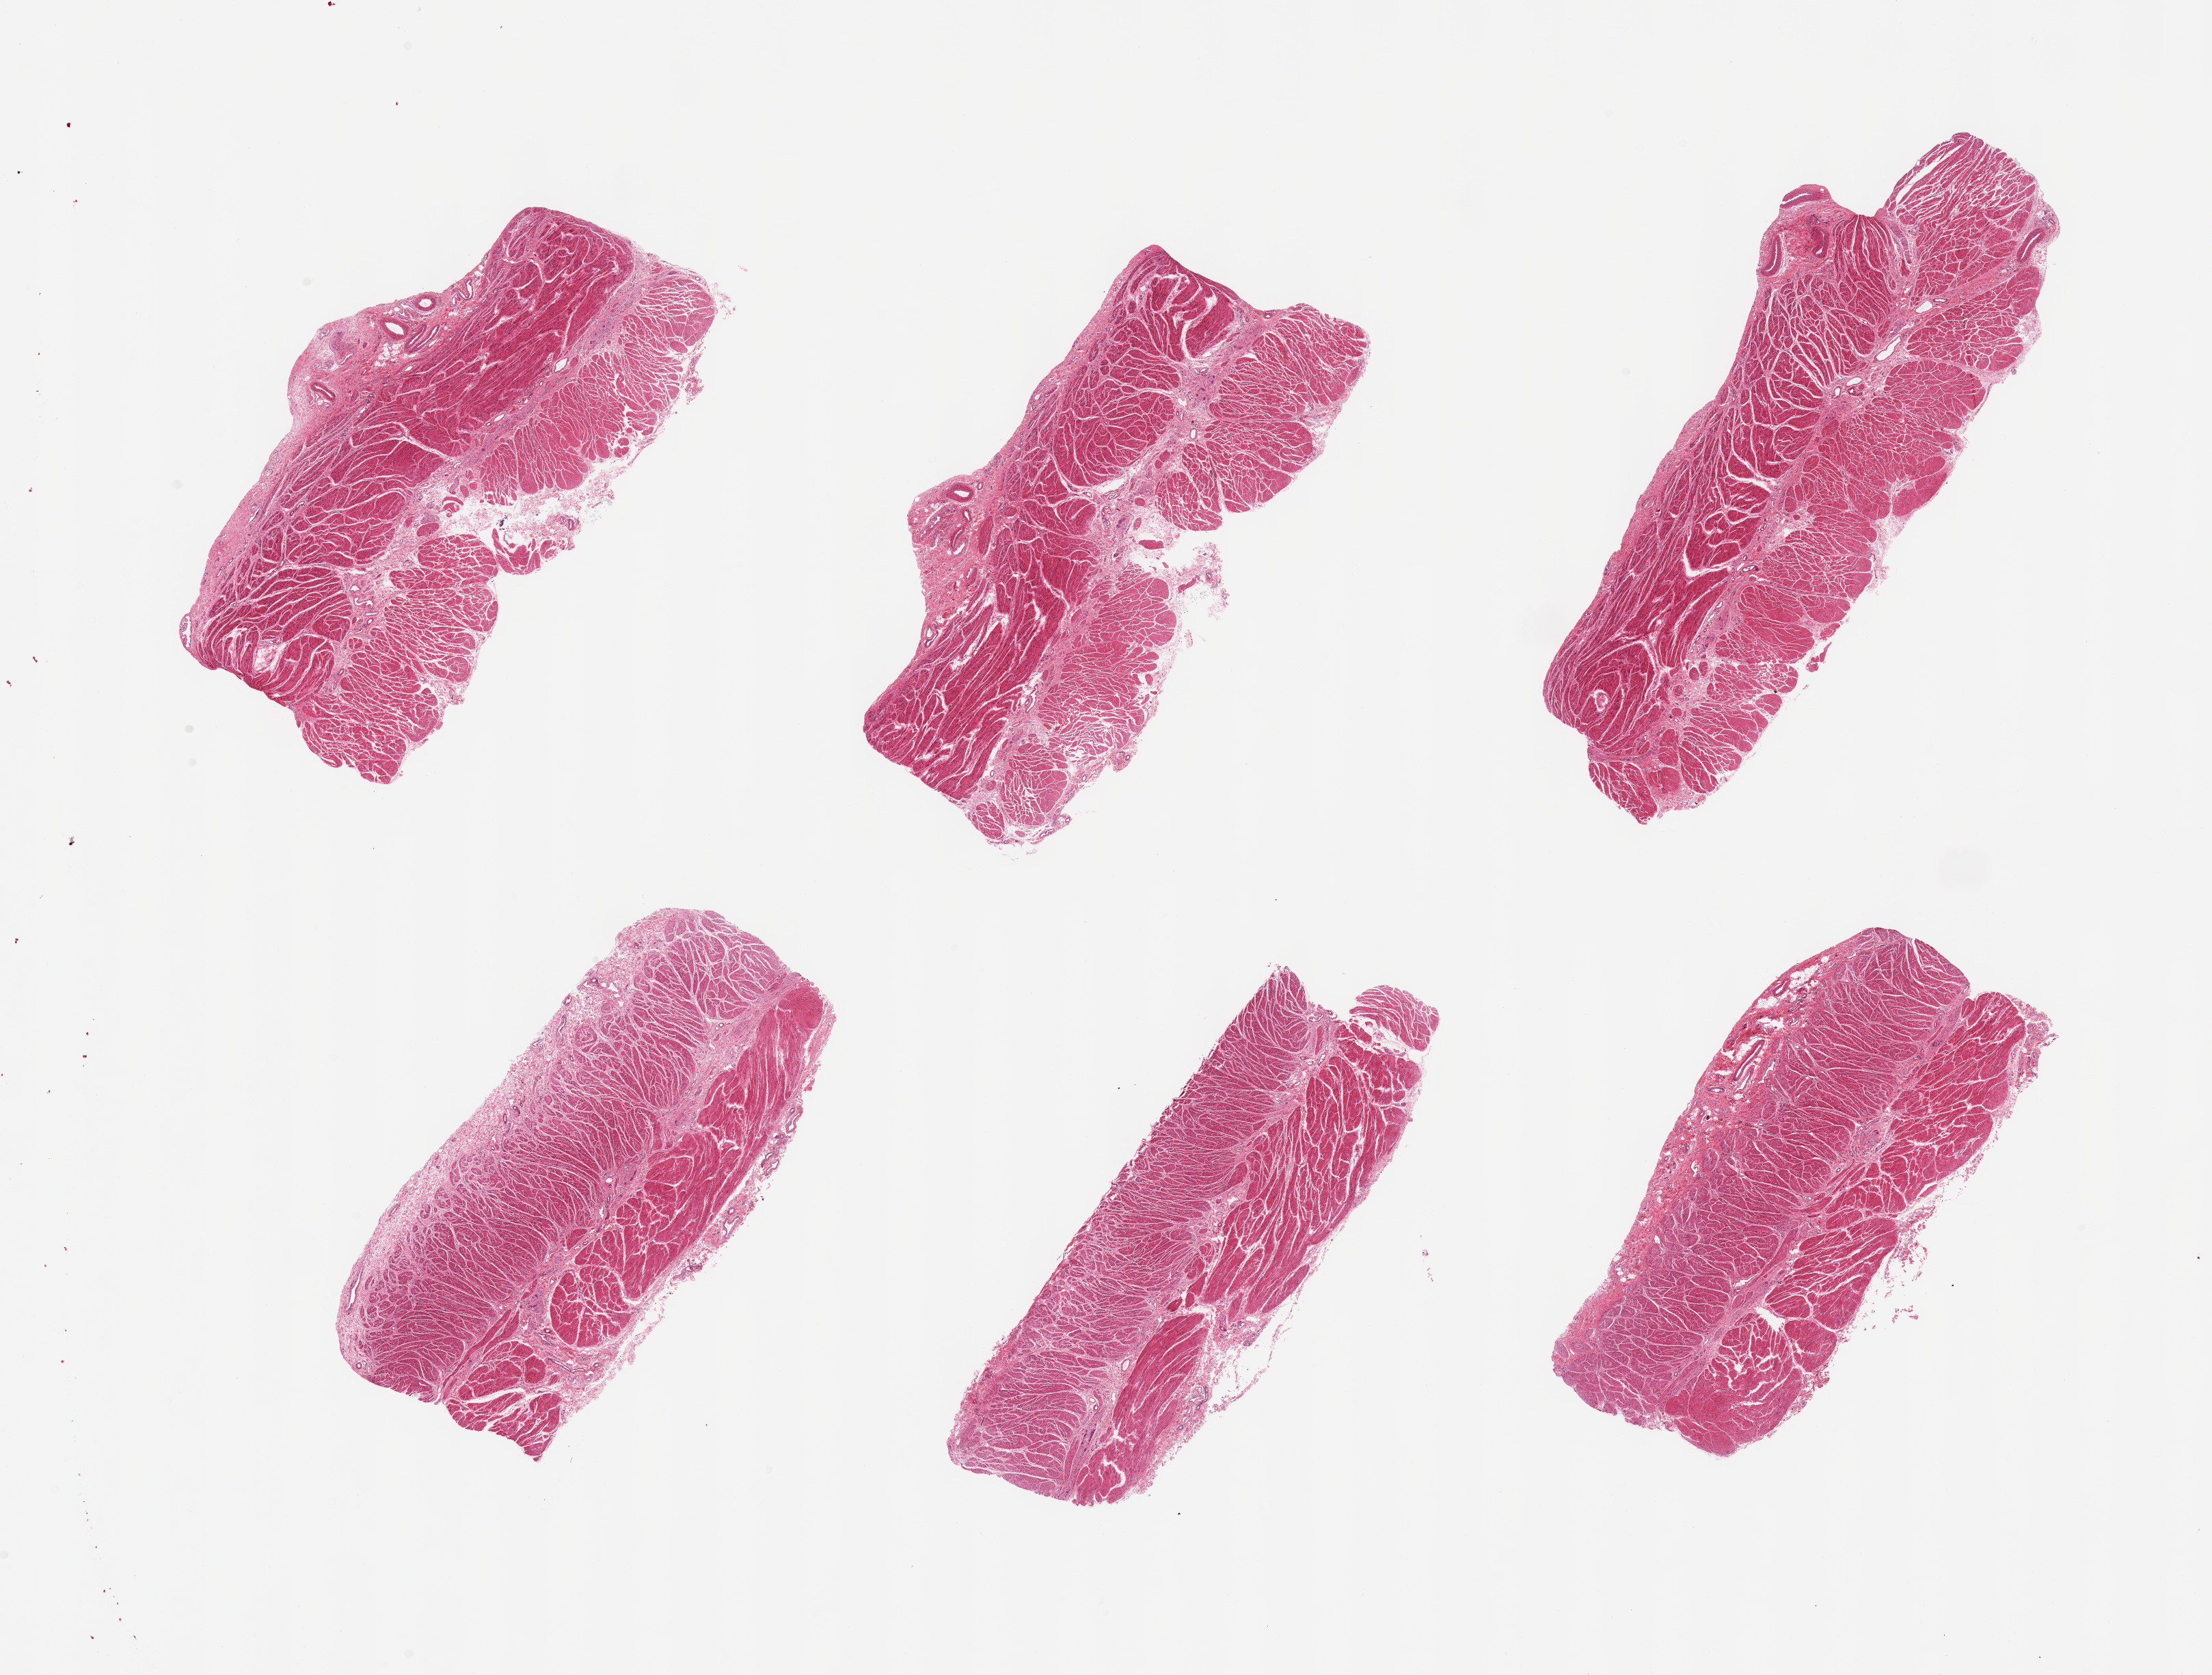
Digitized haematoxylin and eosin-stained section — shown as a low-resolution overview of the whole scanned area (about 25.6 x 19.4 mm, from a 20x scan); PAXgene-fixed, paraffin-embedded tissue; target tissue: gastroesophageal junction; tissue donor sample. Female donor.
Pathologist's review note for this sample: 6 pieces, confirmed target muscularis.